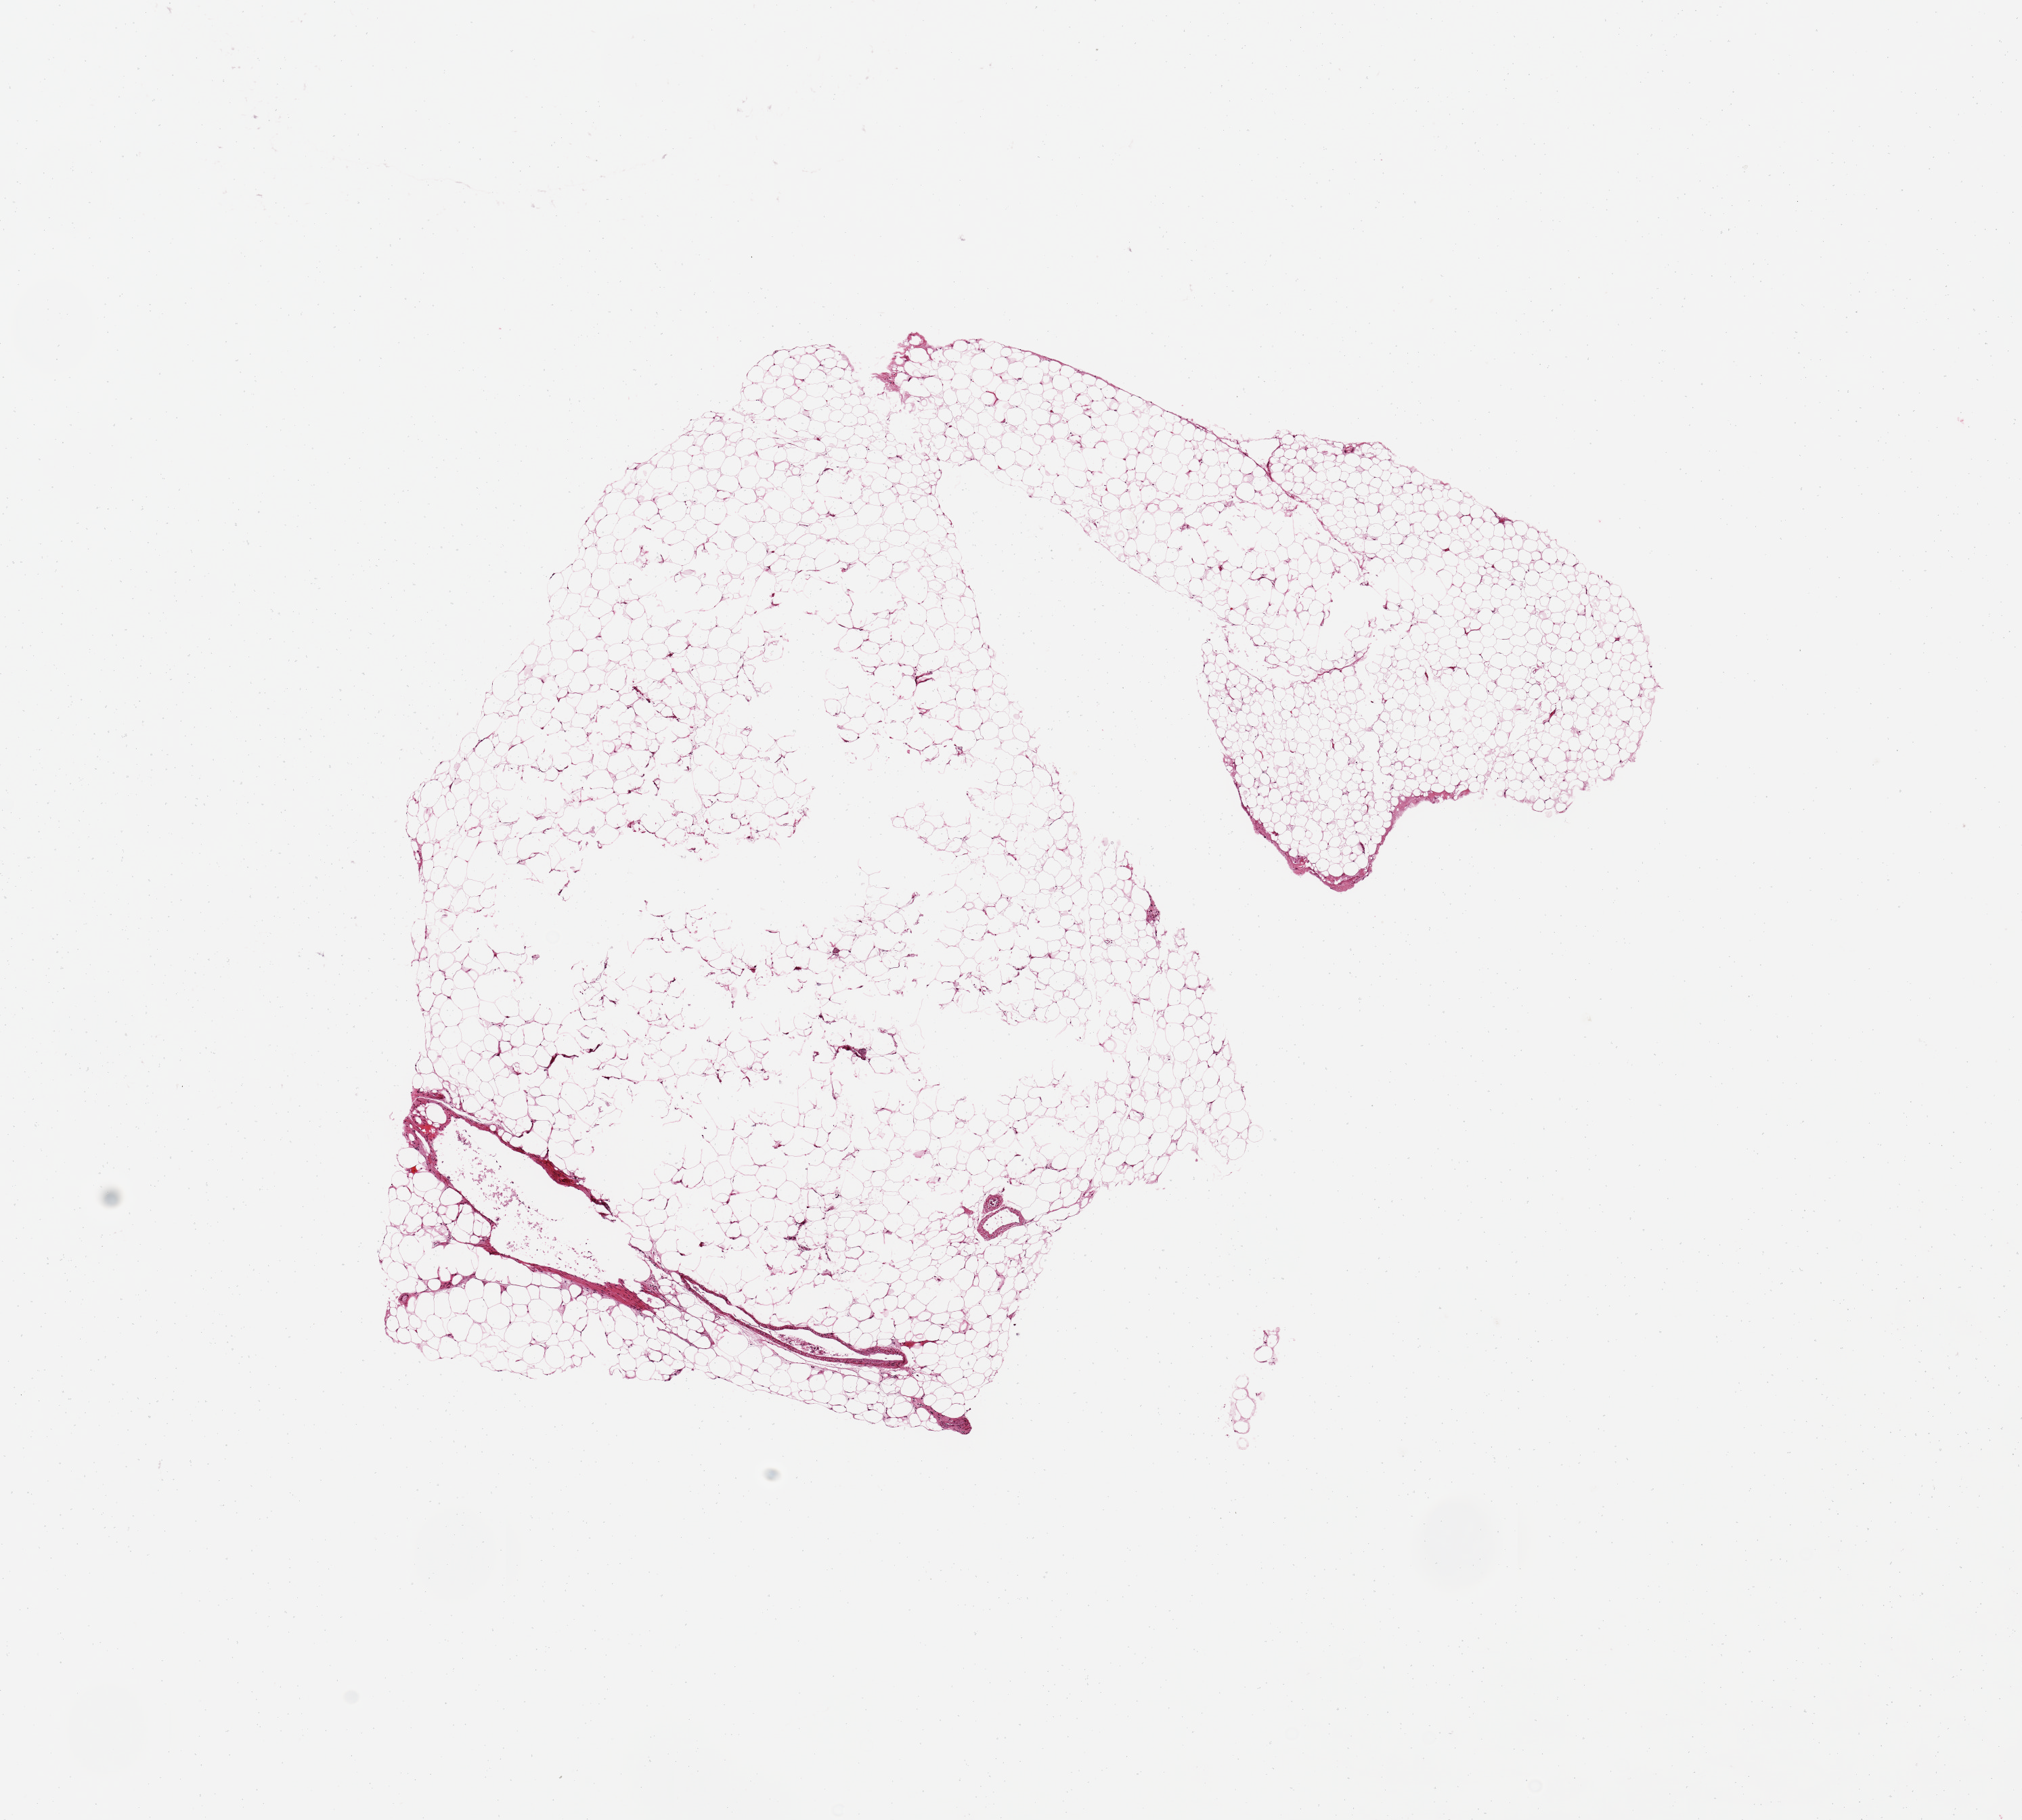
Whole-slide image, hematoxylin and eosin (H&E) stain, low-resolution overview of the scanned area, about 11.8 x 10.6 mm (acquisition: 20x scan); PAXgene-fixed, paraffin-embedded tissue; sampled site (target tissue): pancreas; donor tissue sample. Donor sex: female.
- pathologist's review note for this sample: Under -fixed adipose tissue only, no pancreas